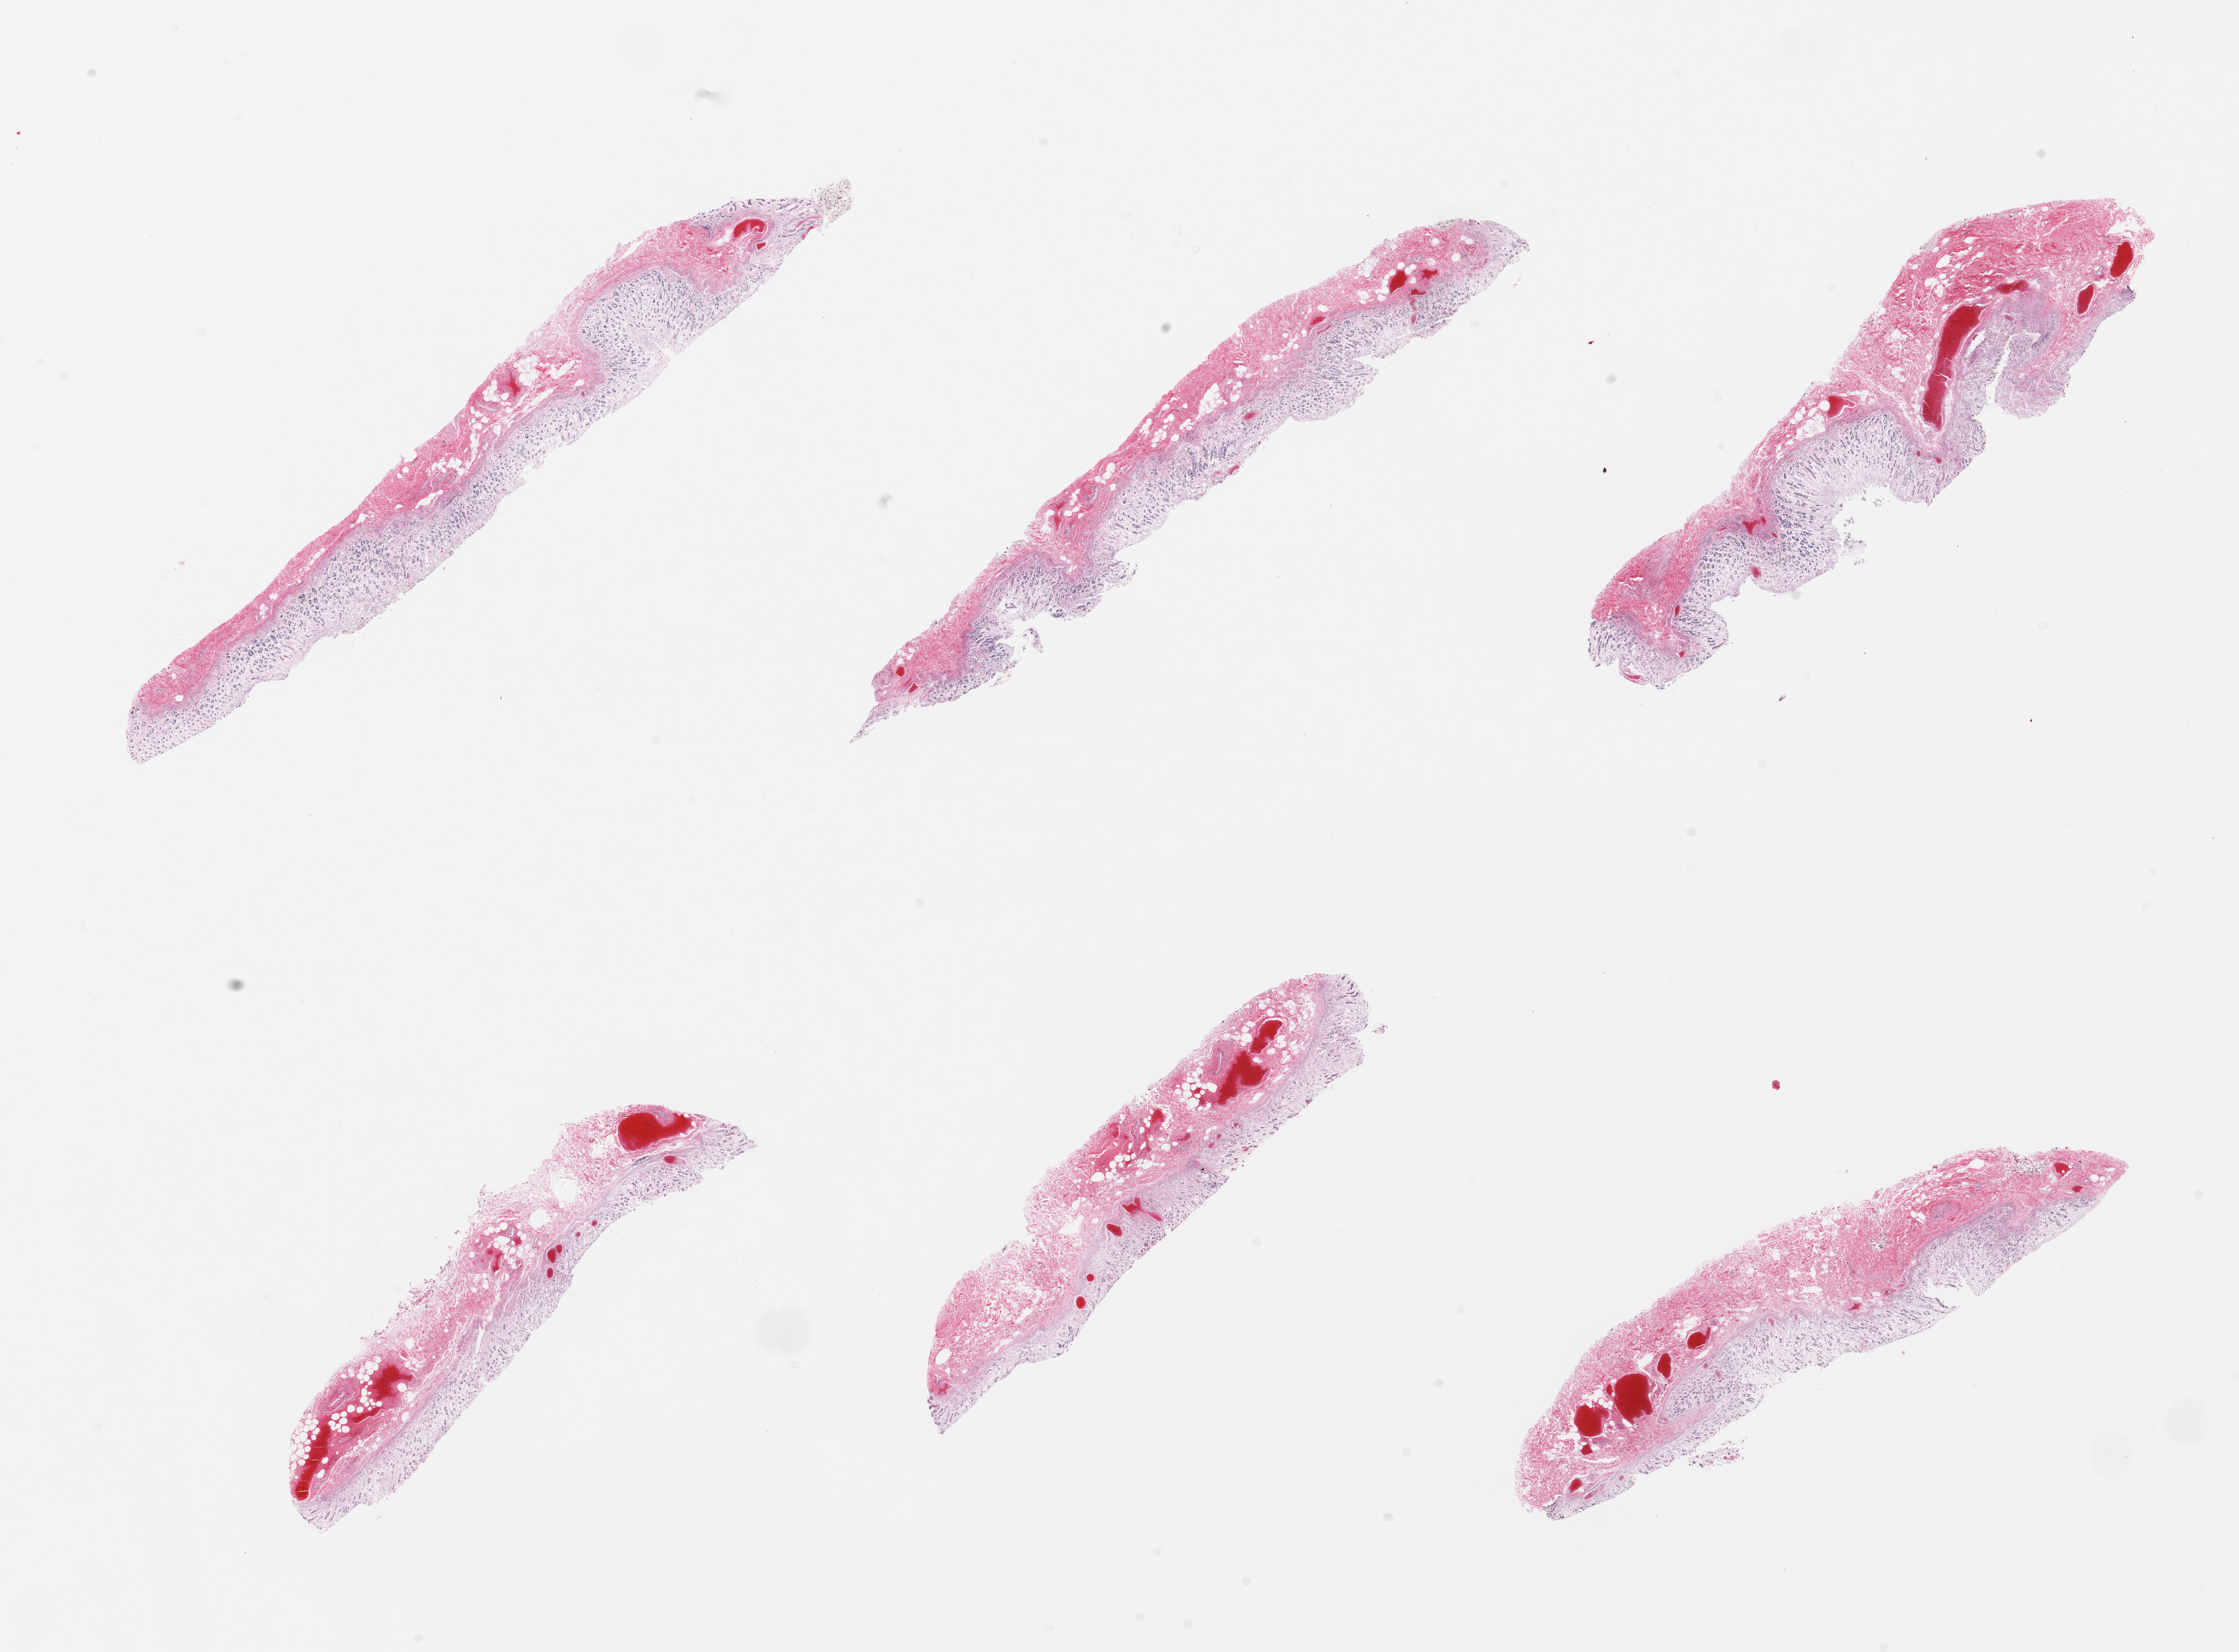
Whole-slide image, H&E stain, low-resolution overview of the scanned area, about 25.6 x 18.9 mm; PAXgene-fixed paraffin-embedded (PFPE) section; sampled site (target tissue): stomach; donor tissue sample. Male donor.
Pathologist's review note for this sample: 6 pieces, mucosa up to ~80% thickness but totally autolyzed.